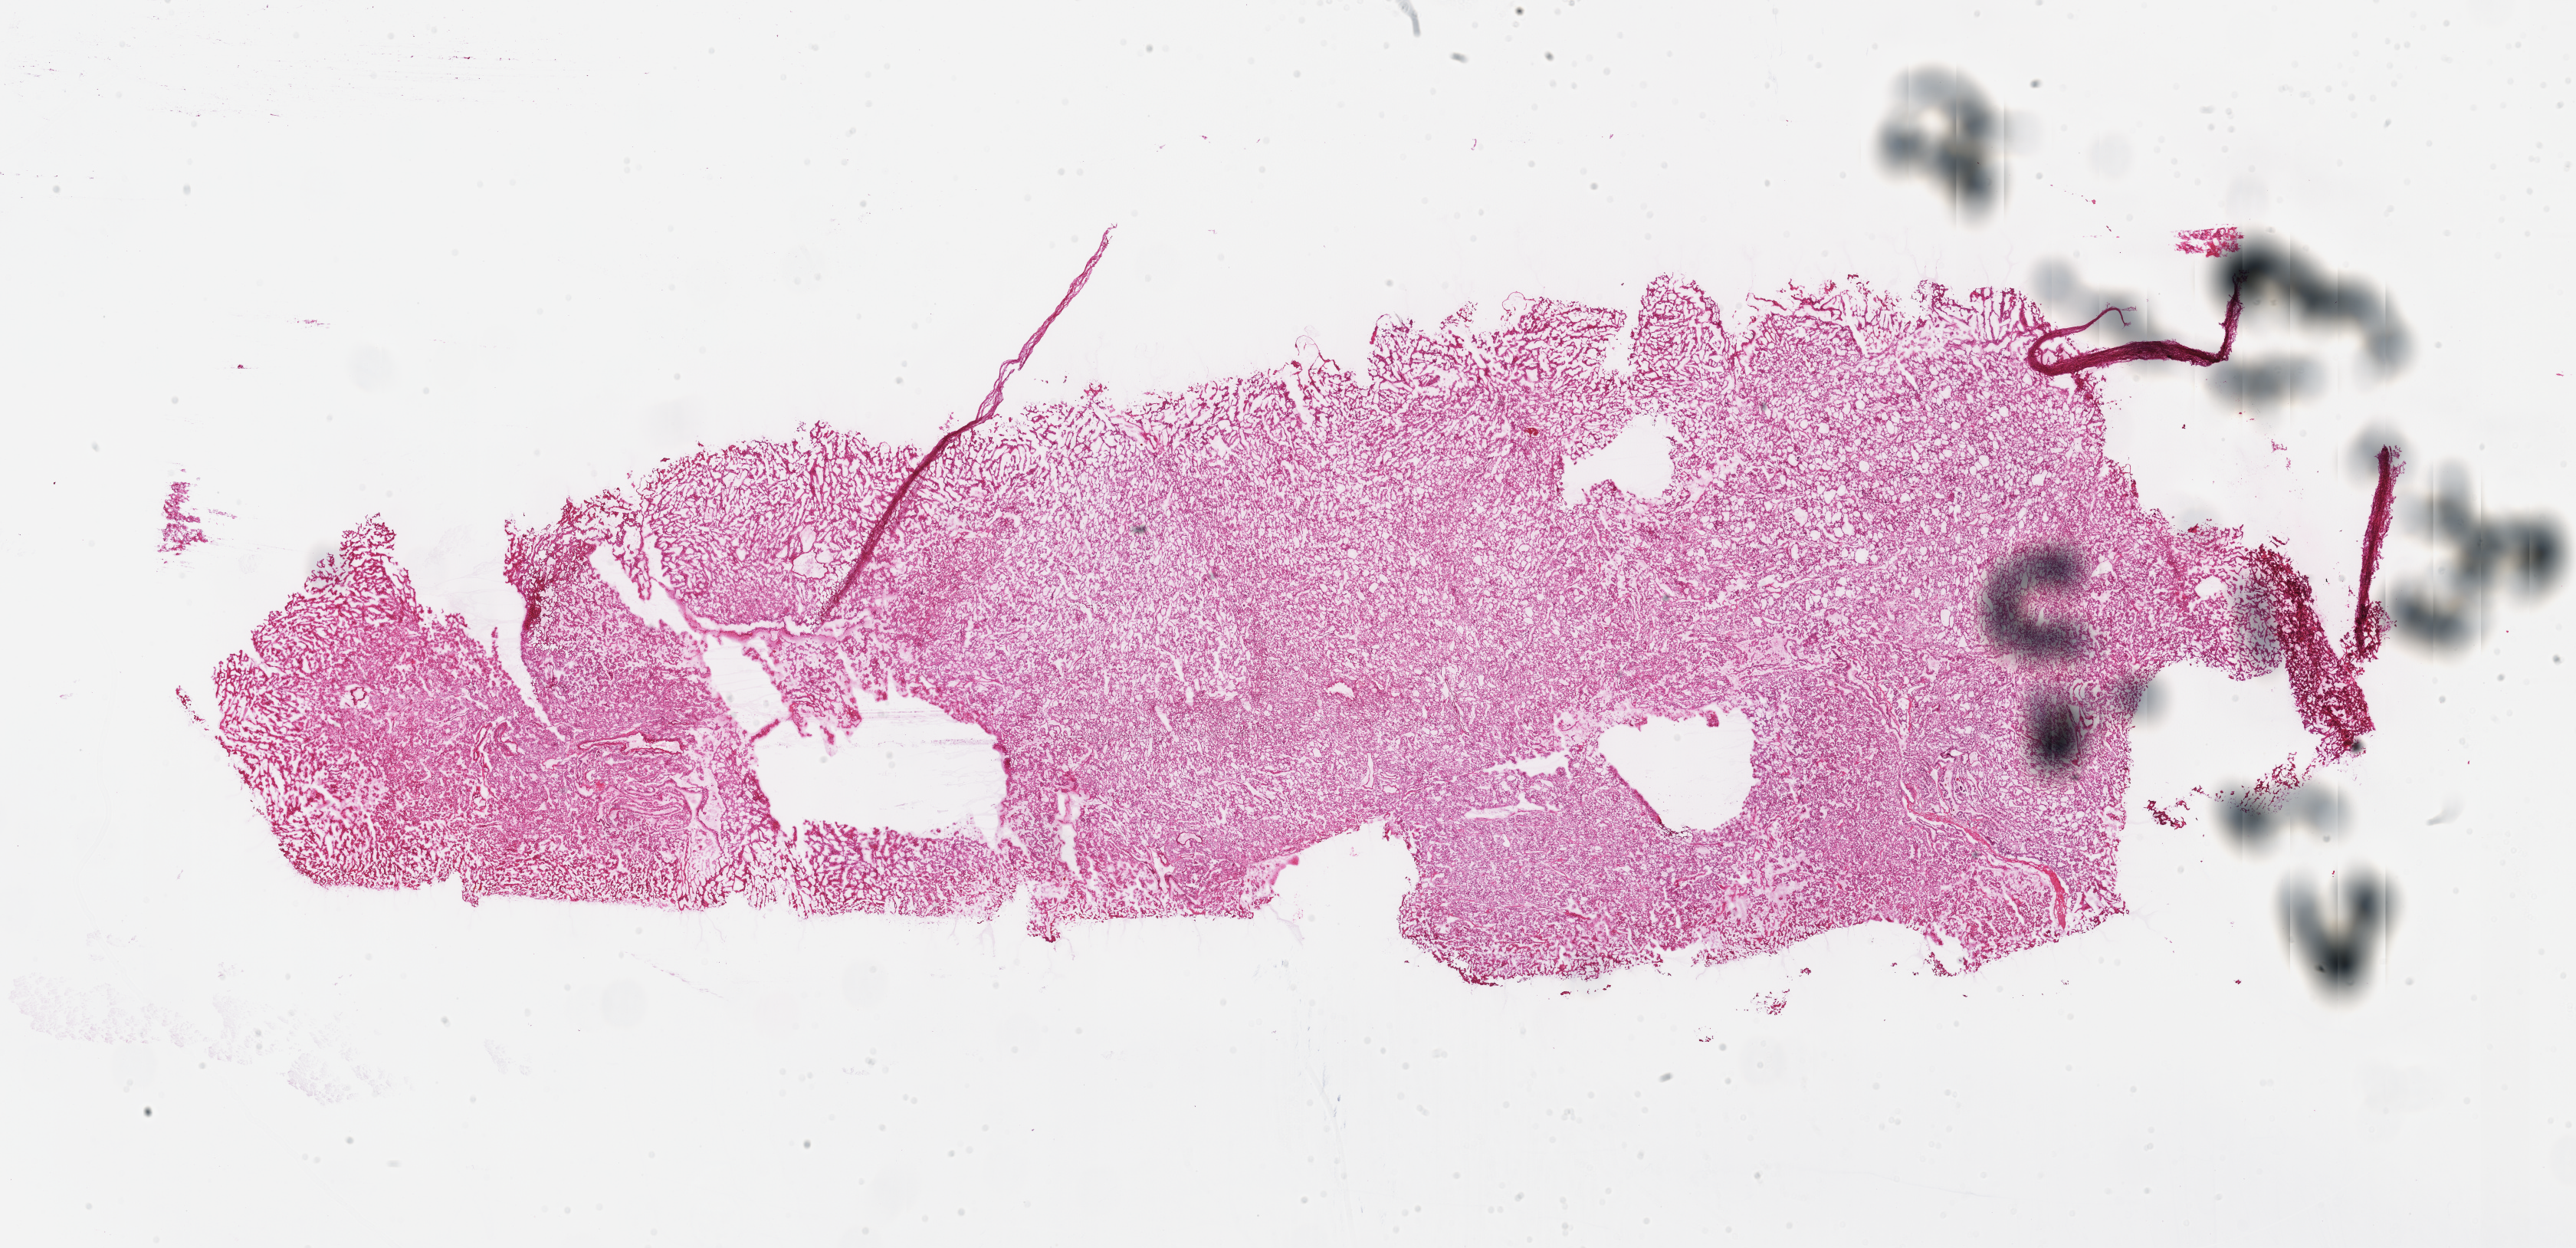
H&E-stained whole-slide image, shown as a low-resolution overview of the whole scanned area (about 26.4 x 12.8 mm, from a 40x scan). Frozen section. Sample: primary tumour, kidney. Female, age 30 years at initial diagnosis. Slide review estimates, as recorded: tumour cells 90%, tumour nuclei 90%, normal cells 0%, stromal cells 10%, necrosis 0%.
Histologic diagnosis: Renal cell carcinoma, chromophobe type. TNM: T1 N0 M0. AJCC pathologic stage: I (7th edition).